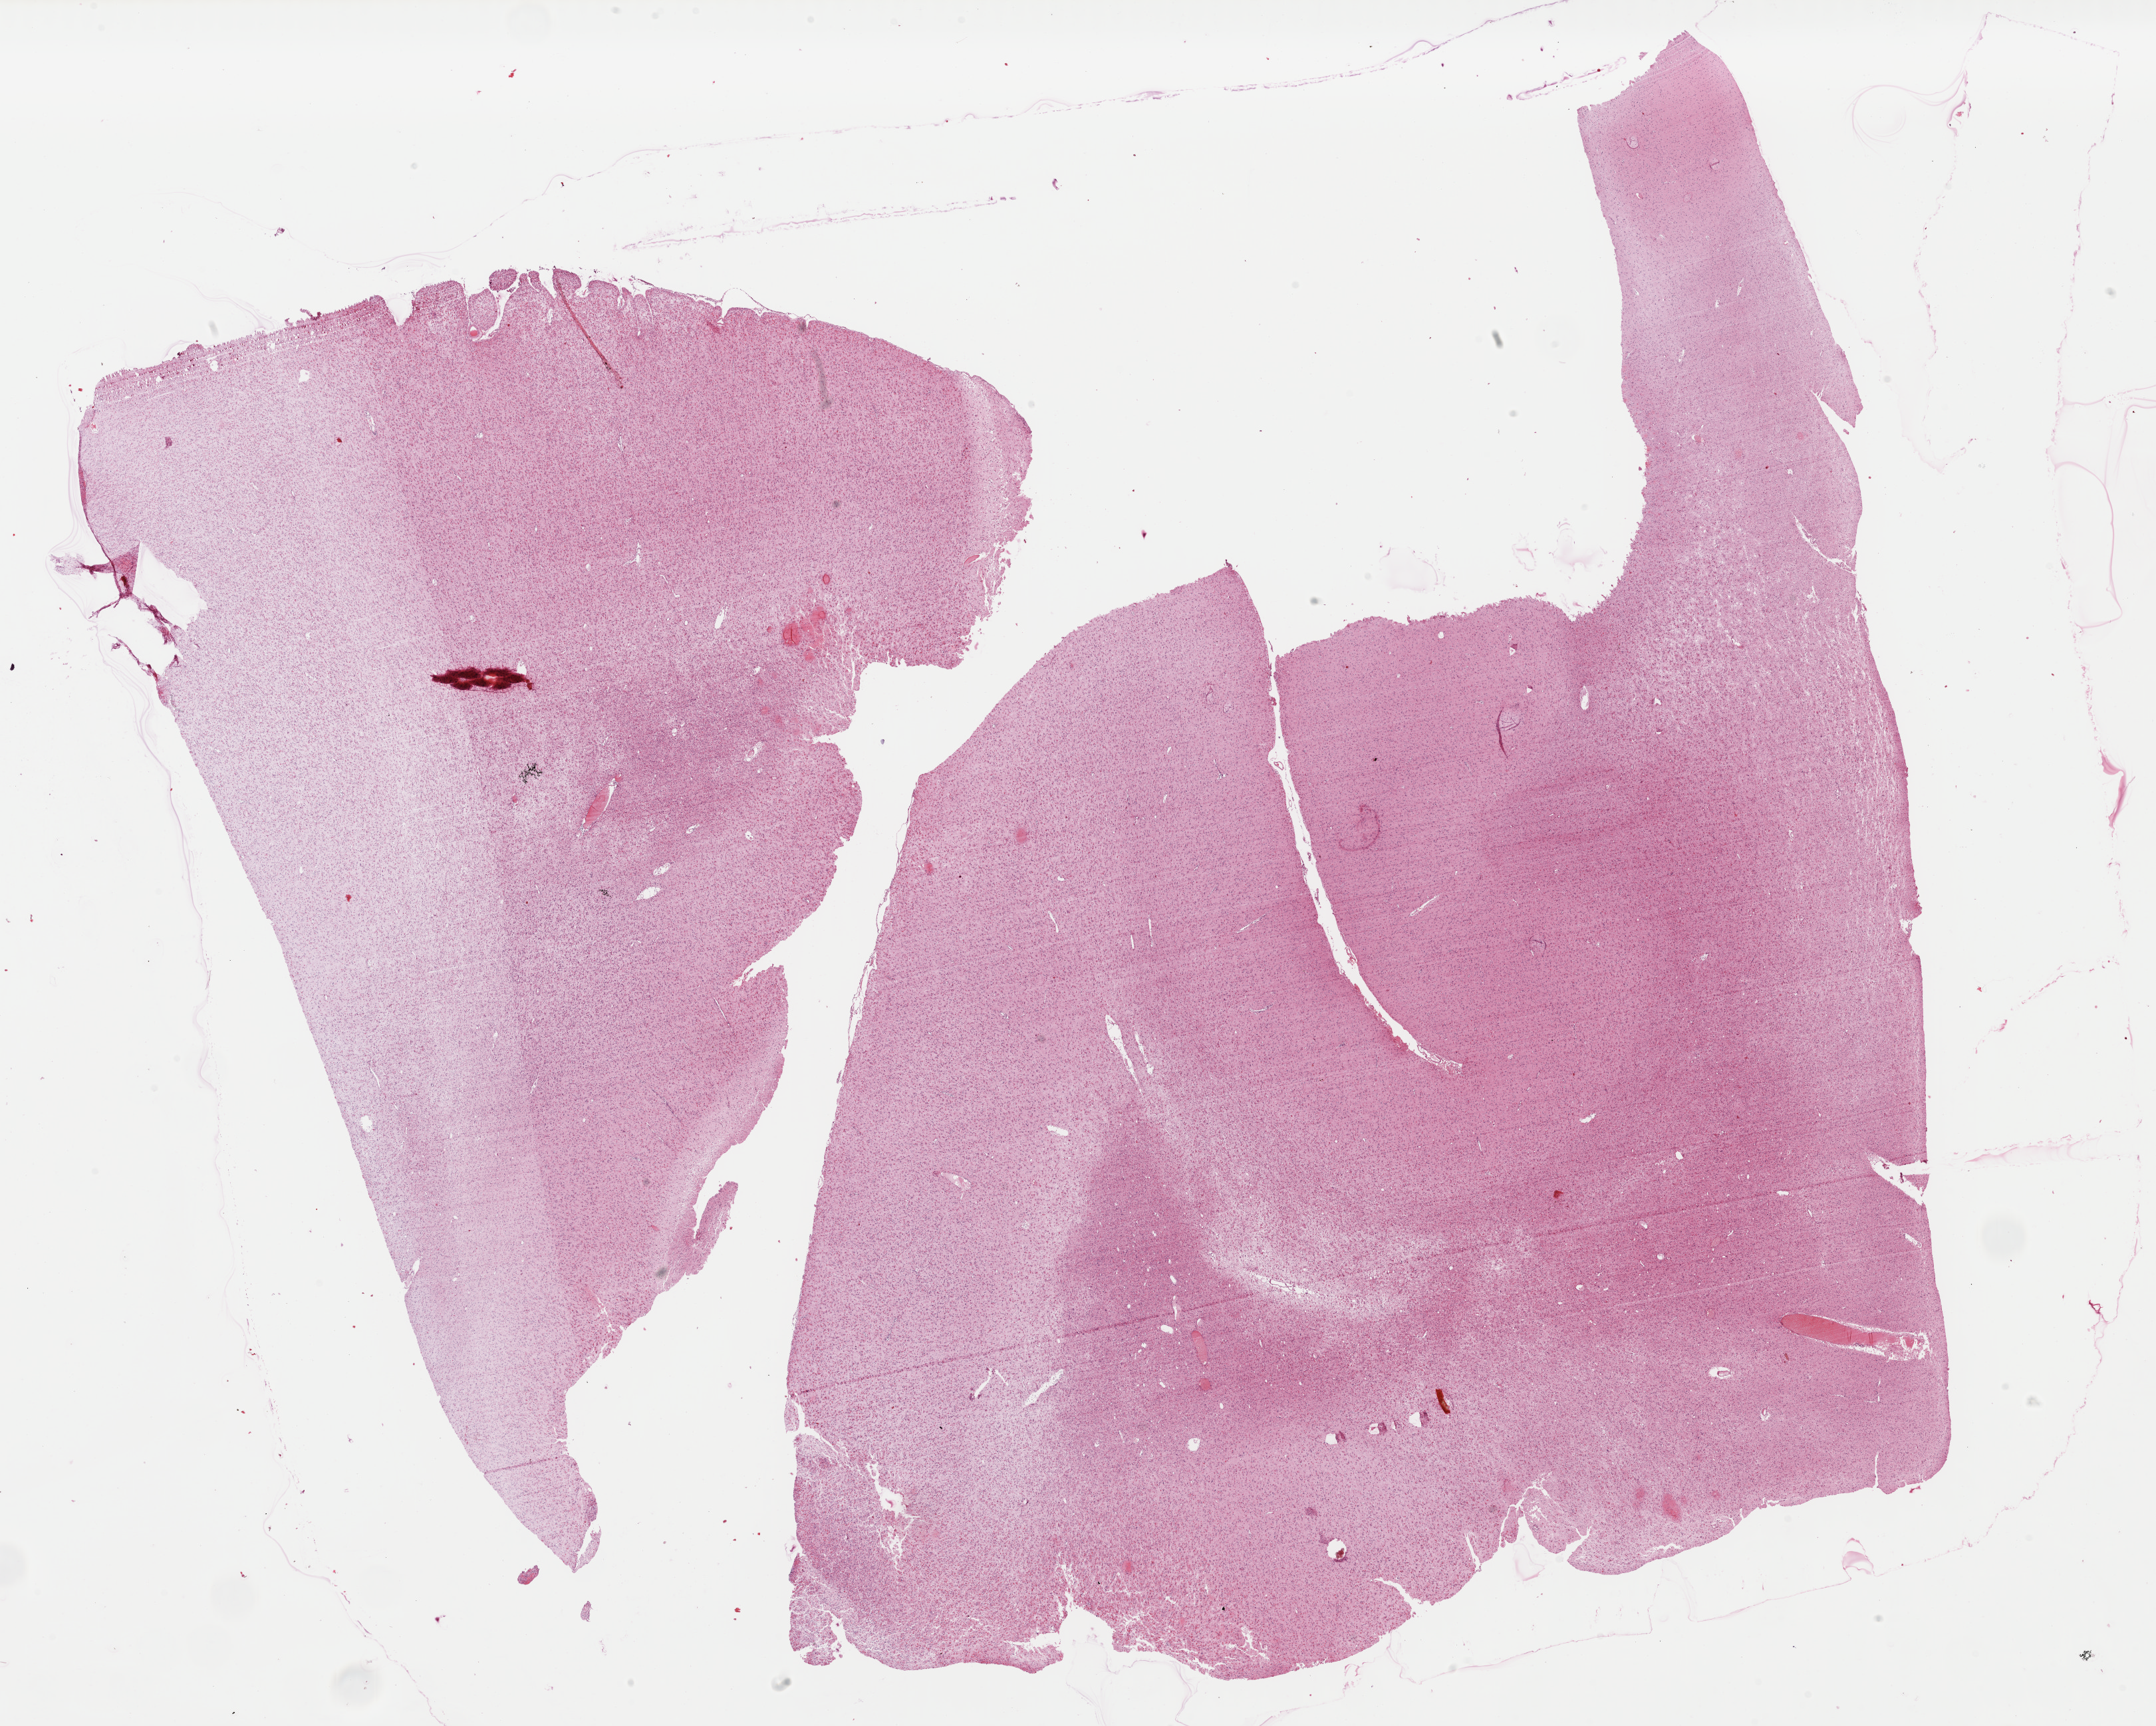
Digitized H&E tissue section (whole slide) — whole scanned area (about 25.6 x 20.5 mm, acquisition: 40x scan) shown as a low-resolution overview; formalin-fixed paraffin-embedded (FFPE) diagnostic section; sample: primary tumour, brain. Patient: male, age at initial diagnosis 66 years. Histologic grade: G2 (moderately differentiated).
* pathologic diagnosis: Astrocytoma, NOS (cerebrum)